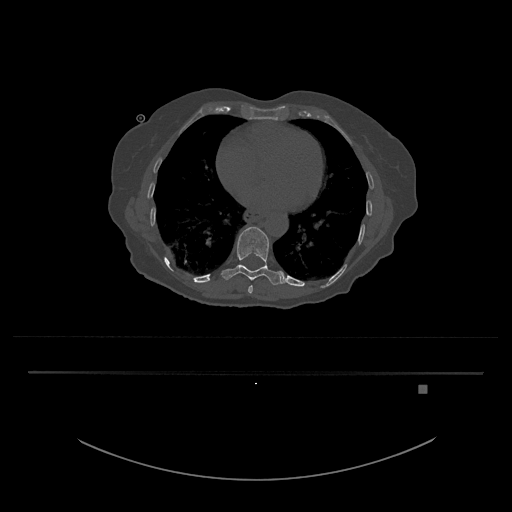
CT including the spine, one axial slice. Slice 717 of 797 in the series (ordered by position). Bone window (W 1800 / L 400 HU). 0.5 mm slice thickness. 512 × 512 image matrix, field of view 500 × 500 mm. Female patient, age 57 years. Case-level facts recorded for this patient, not image findings: primary cancer: cervical.
Structures marked on this image (semi-automatically segmented with operator editing):
- T10 vertebra: box from (x=221, y=226) to (x=284, y=285) px
- T9 vertebra: (x=248, y=285)–(x=253, y=294)